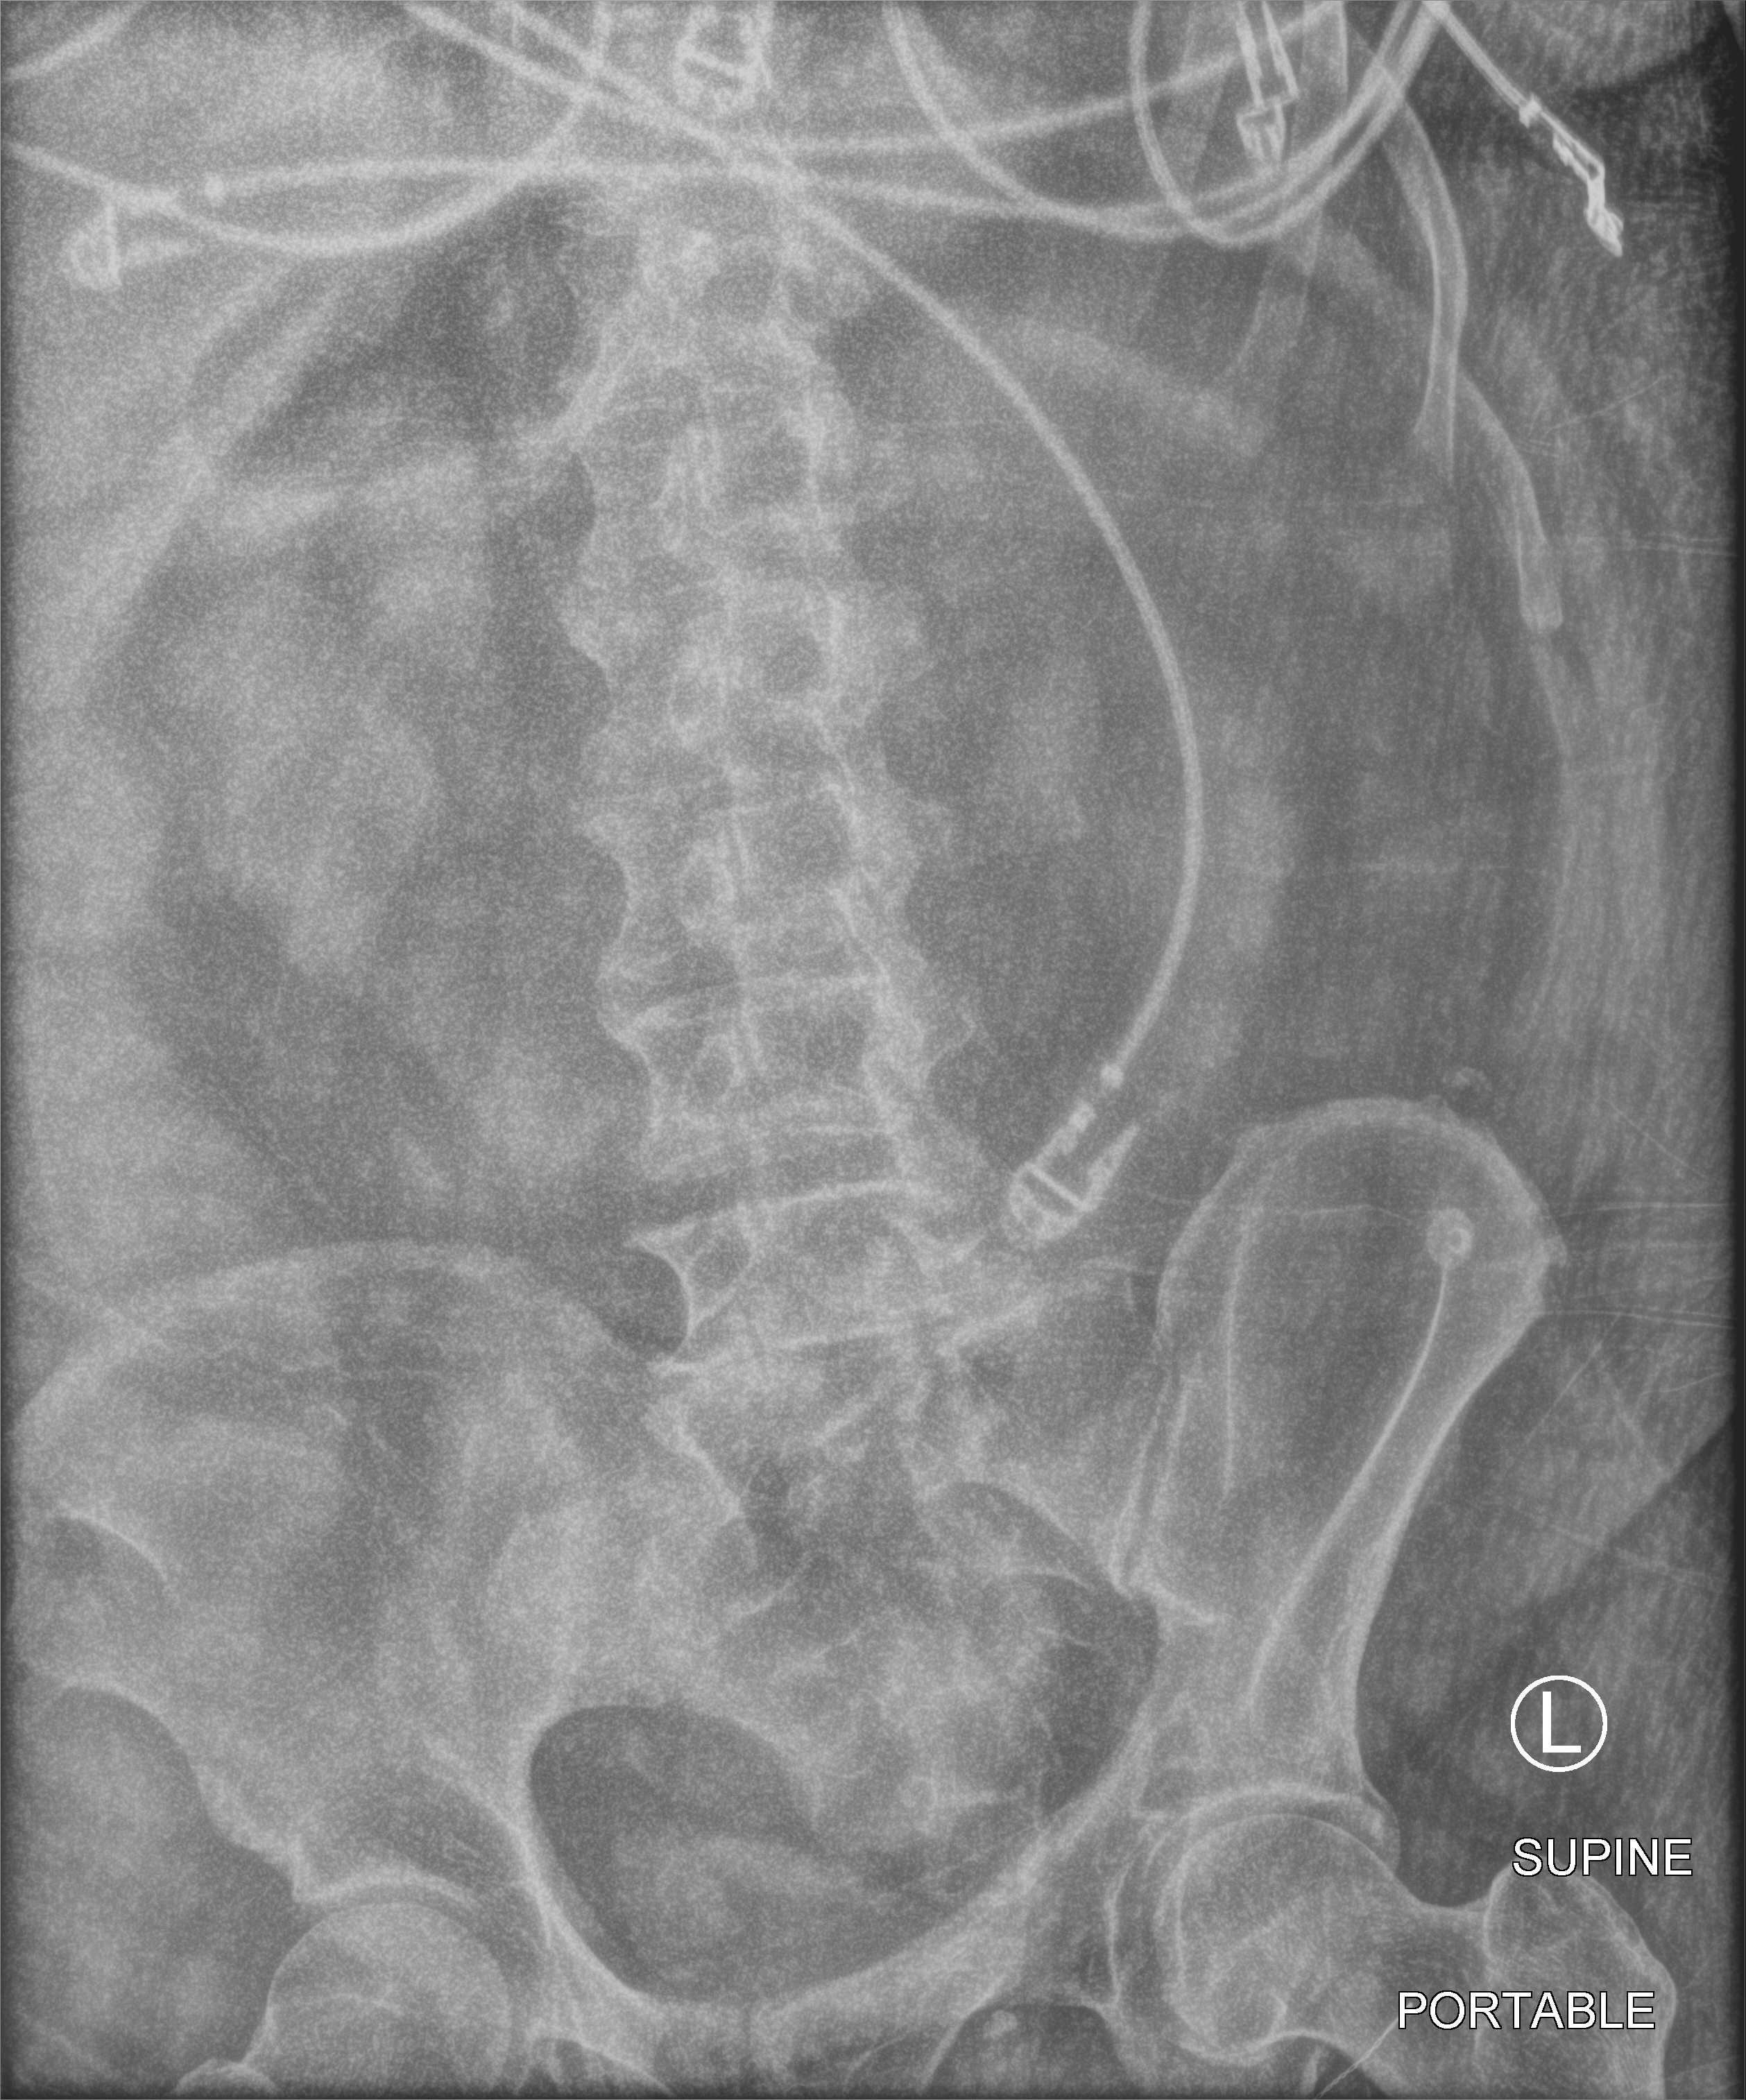
Bedside abdomen radiograph (computed radiography); anteroposterior (AP) projection. Male patient hospitalised with COVID-19, age 60–74 years.
From the hospital-stay record, not from the radiograph (when in the stay this image was taken is not recorded): other chronic lung disease (admission record): no; admitted to intensive care during this hospital stay: yes; length of hospital stay: 20 days.